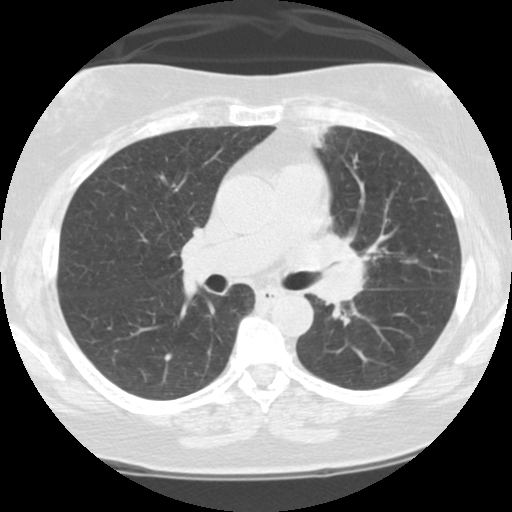
Axial slice from a low-dose chest CT screening exam, third annual screen, lung window (W 1500 / L -600 HU), 2.5 mm slice thickness, slice 45 of 108 in the series, 512 × 512 image matrix, field of view 300 × 300 mm. Female participant, aged 59 years at enrolment. Current smoker at enrolment.
Expert reader's lesion annotation, bounding box [x1, y1, x2, y2] px = [285, 213, 387, 325]. No non-calcified nodule or mass ≥4 mm was recorded by the screening reader at this exam. Official screen result: positive, other. Lung cancer was diagnosed 192 days after this screen: small cell carcinoma, NOS, left upper lobe, left hilum, mediastinum, left main stem bronchus, stage IV (AJCC 6th edition), 63 mm at pathology.